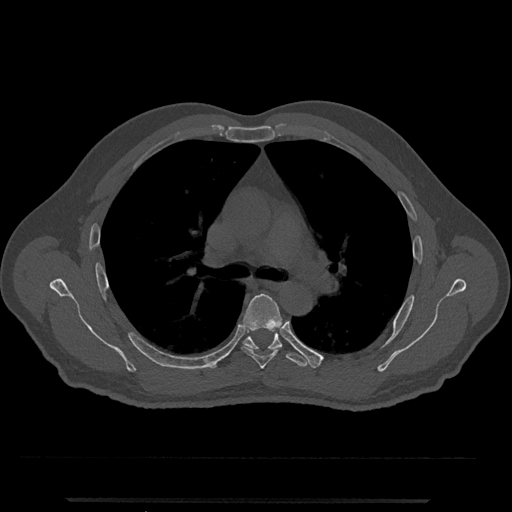
CT including the spine, one axial slice; slice 770 of 797 in the series (ordered by position); reconstruction kernel Br40s/3; 120 kVp; bone window (W 1800 / L 400 HU); 0.5 mm slice thickness; 512 × 512 image matrix, field of view 419 × 419 mm. Male patient, age 63 years. Case-level facts recorded for this patient, not image findings: primary cancer: prostate.
Outlined on this slice (semi-automatic segmentation, software-assisted and operator-edited):
- T5 vertebra: box from (x=241, y=293) to (x=282, y=369) px
- T6 vertebra: (x=243, y=333)–(x=307, y=367)